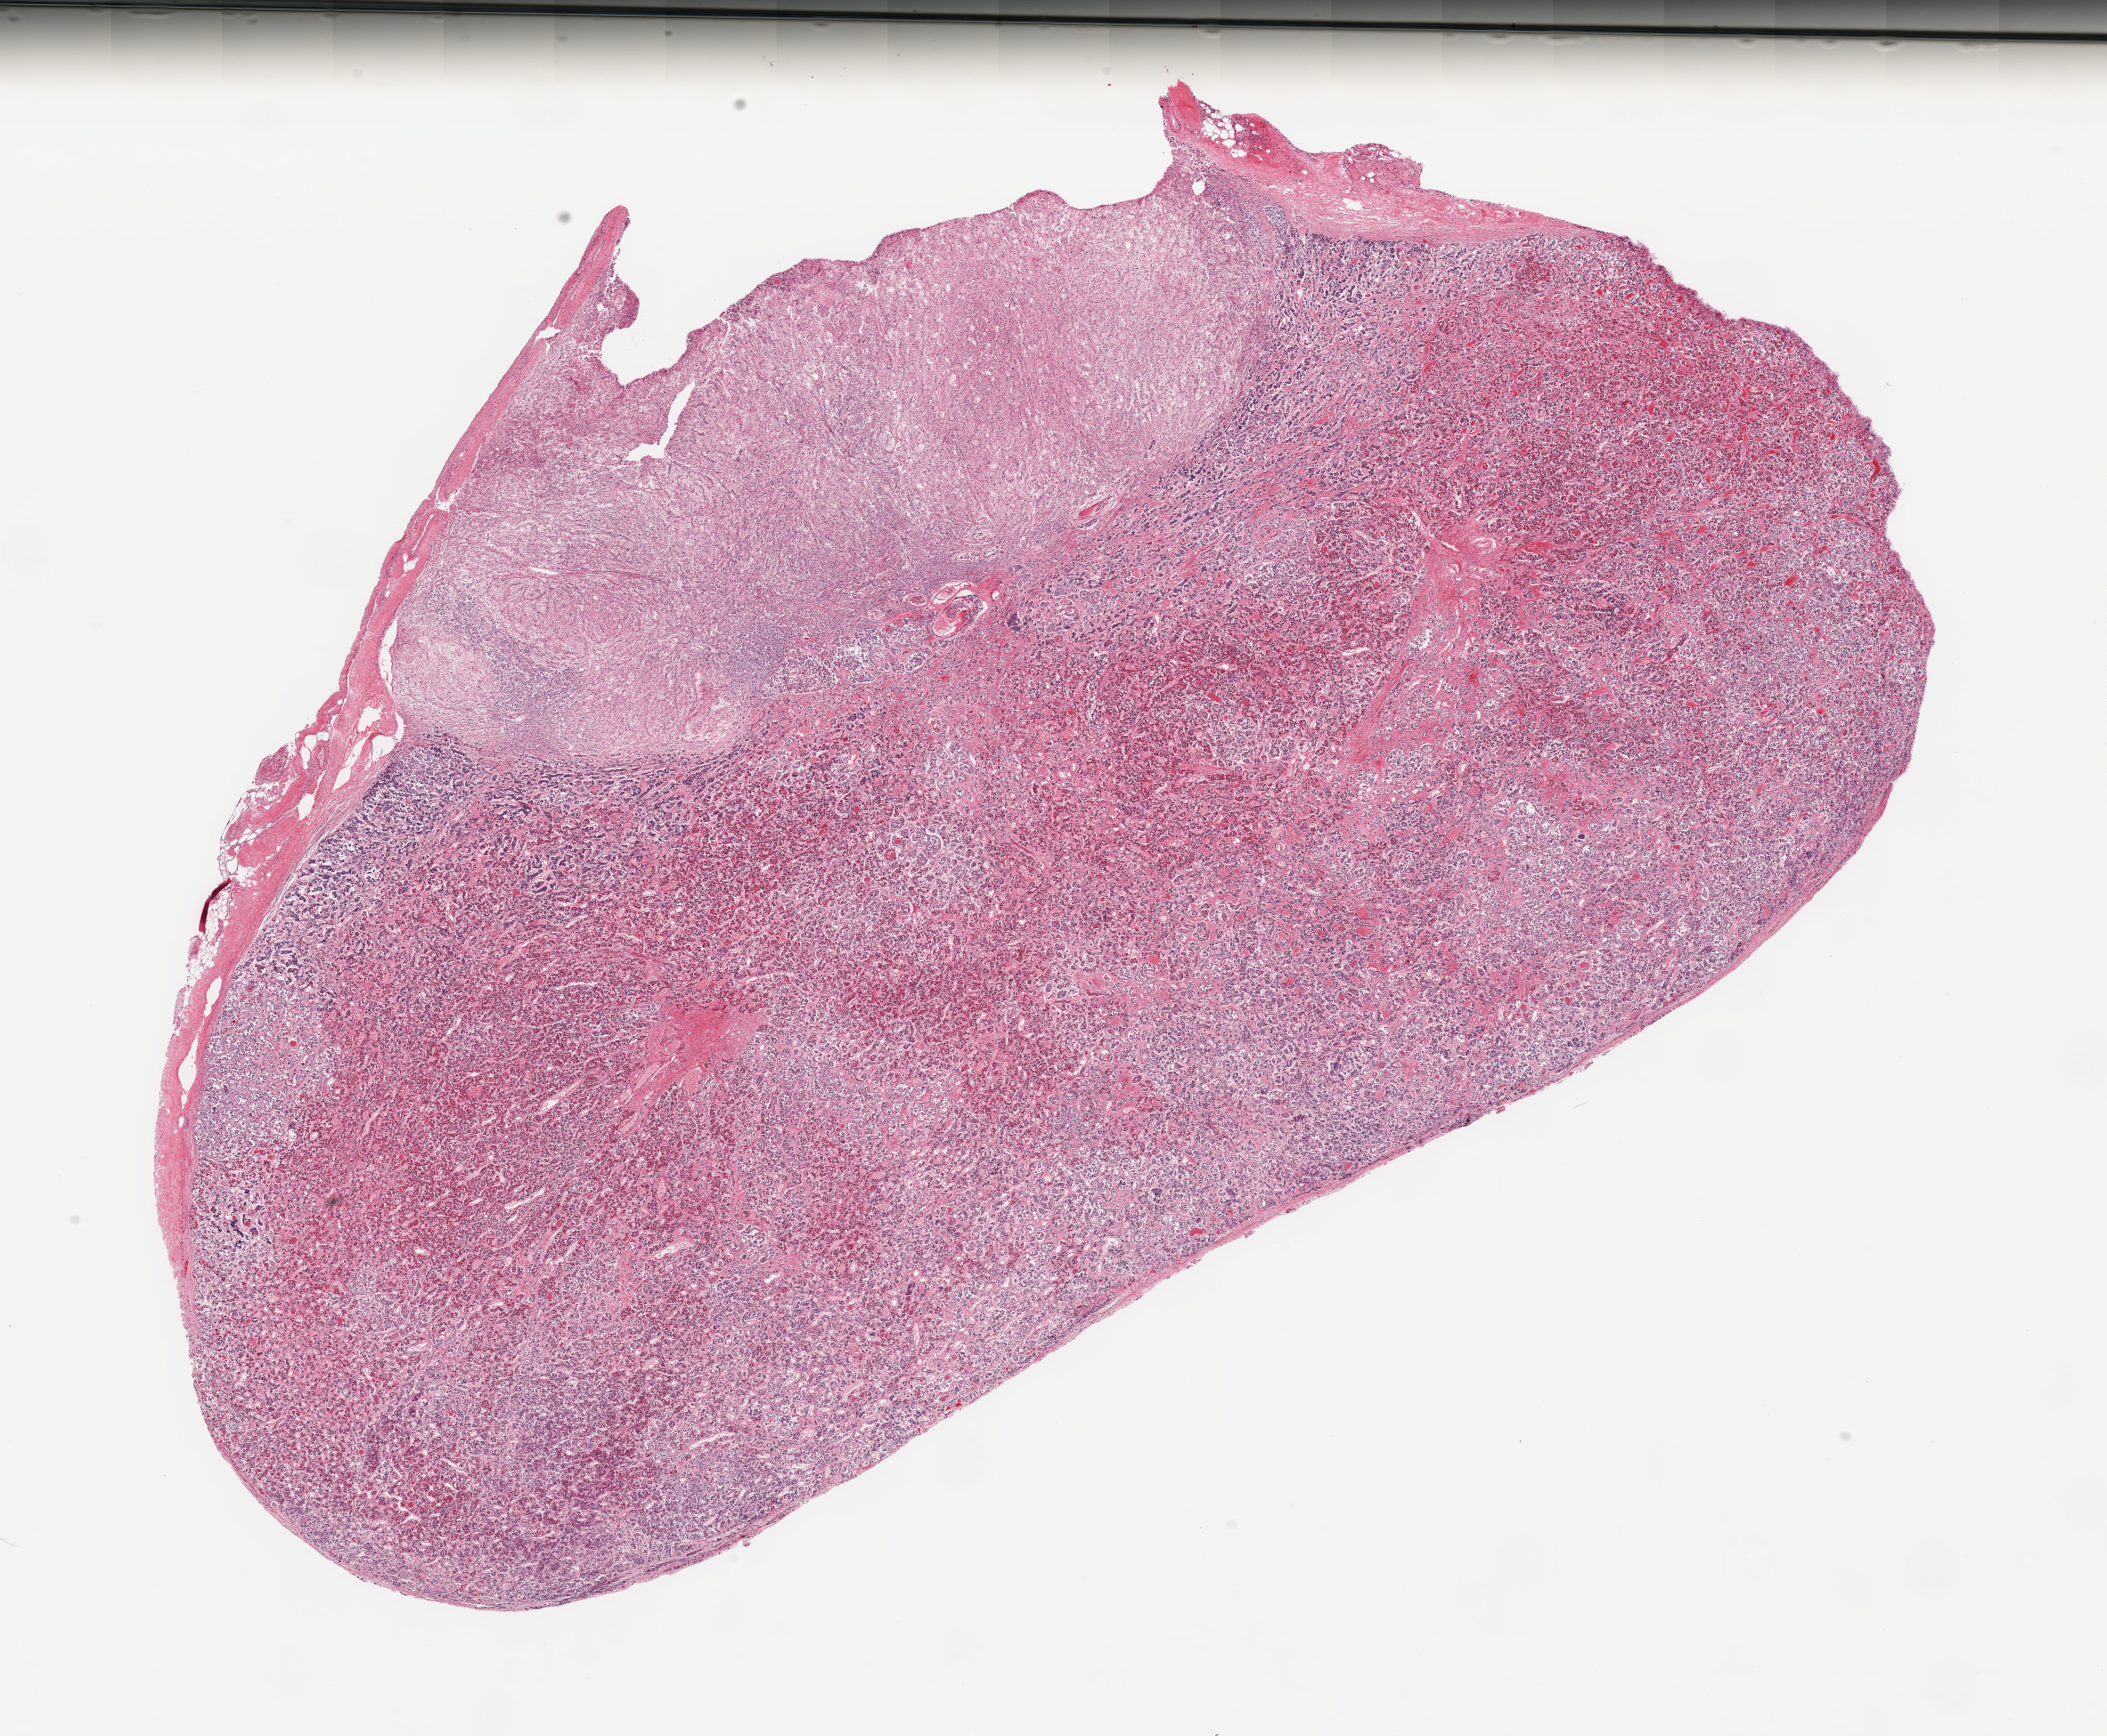
H&E whole-slide image — a low-resolution overview of the entire scanned area, about 18.7 x 15.4 mm (acquisition: 20x scan). PAXgene-fixed paraffin-embedded (PFPE) section. Sampled site (target tissue): pituitary. Tissue donor sample.
Reviewer comment on this tissue sample: 1 piece; moderately autolyzed adenohypophysis and mildly autolyzed neurohypophysis.